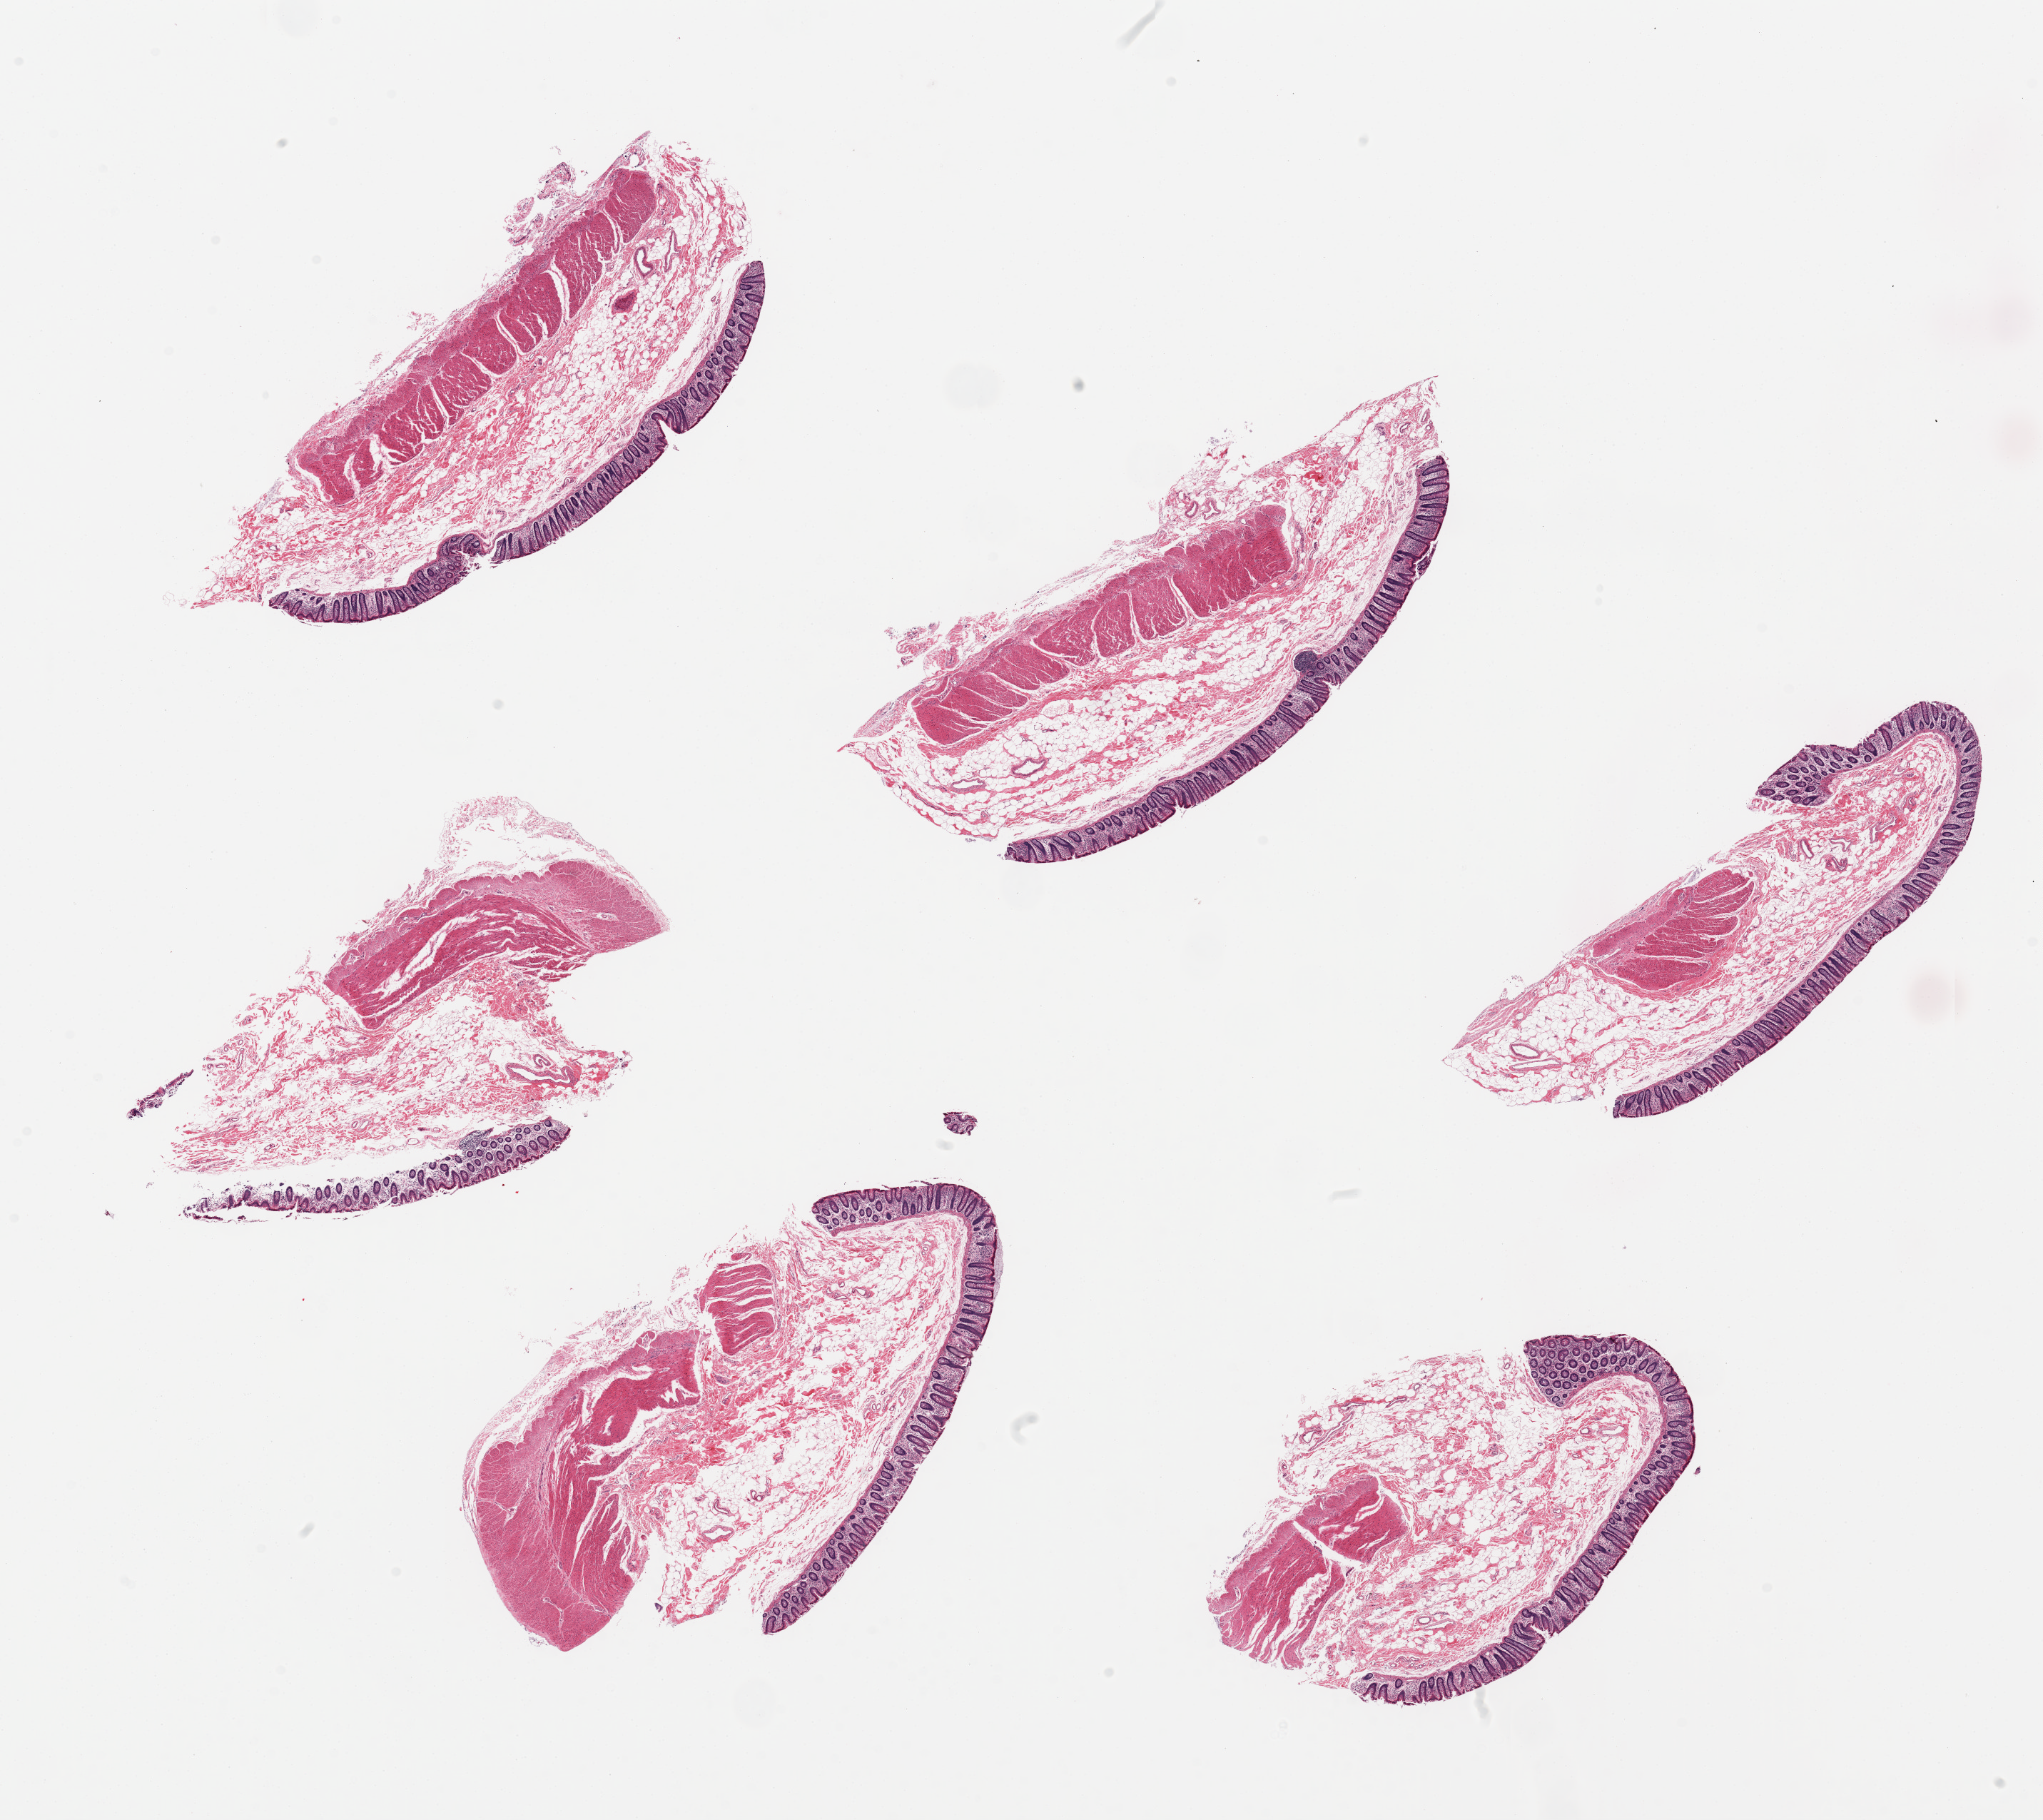
Digitized haematoxylin and eosin-stained section — whole scanned area (about 22.6 x 20.2 mm, from a 20x scan) shown as a low-resolution overview. PAXgene-fixed, paraffin-embedded tissue. Target tissue: transverse colon. Tissue donor sample. Donor: male.
Pathologist's review note for this sample: 6 pieces; full thickness of colonic wall.